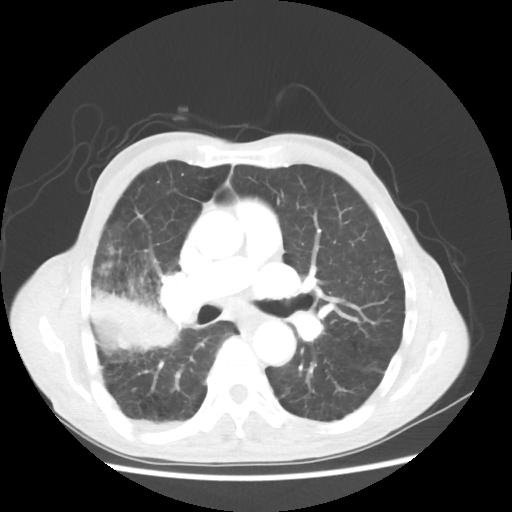
Chest CT, one axial slice; position 30 of 58 along the scan axis; reconstruction kernel STANDARD; lung window (W 1500 / L -600 HU); 5 mm slice thickness; 512 × 512 image matrix, field of view 351 × 351 mm. Patient: male, 75 years. Case-level facts recorded for this patient, not image findings: clinical TNM (as recorded): T4 N1 M1.
Outlined on this slice (rectangle marked by the reading radiologist):
- lung tumour (recorded histology: adenocarcinoma): box from (x=77, y=275) to (x=186, y=358) px